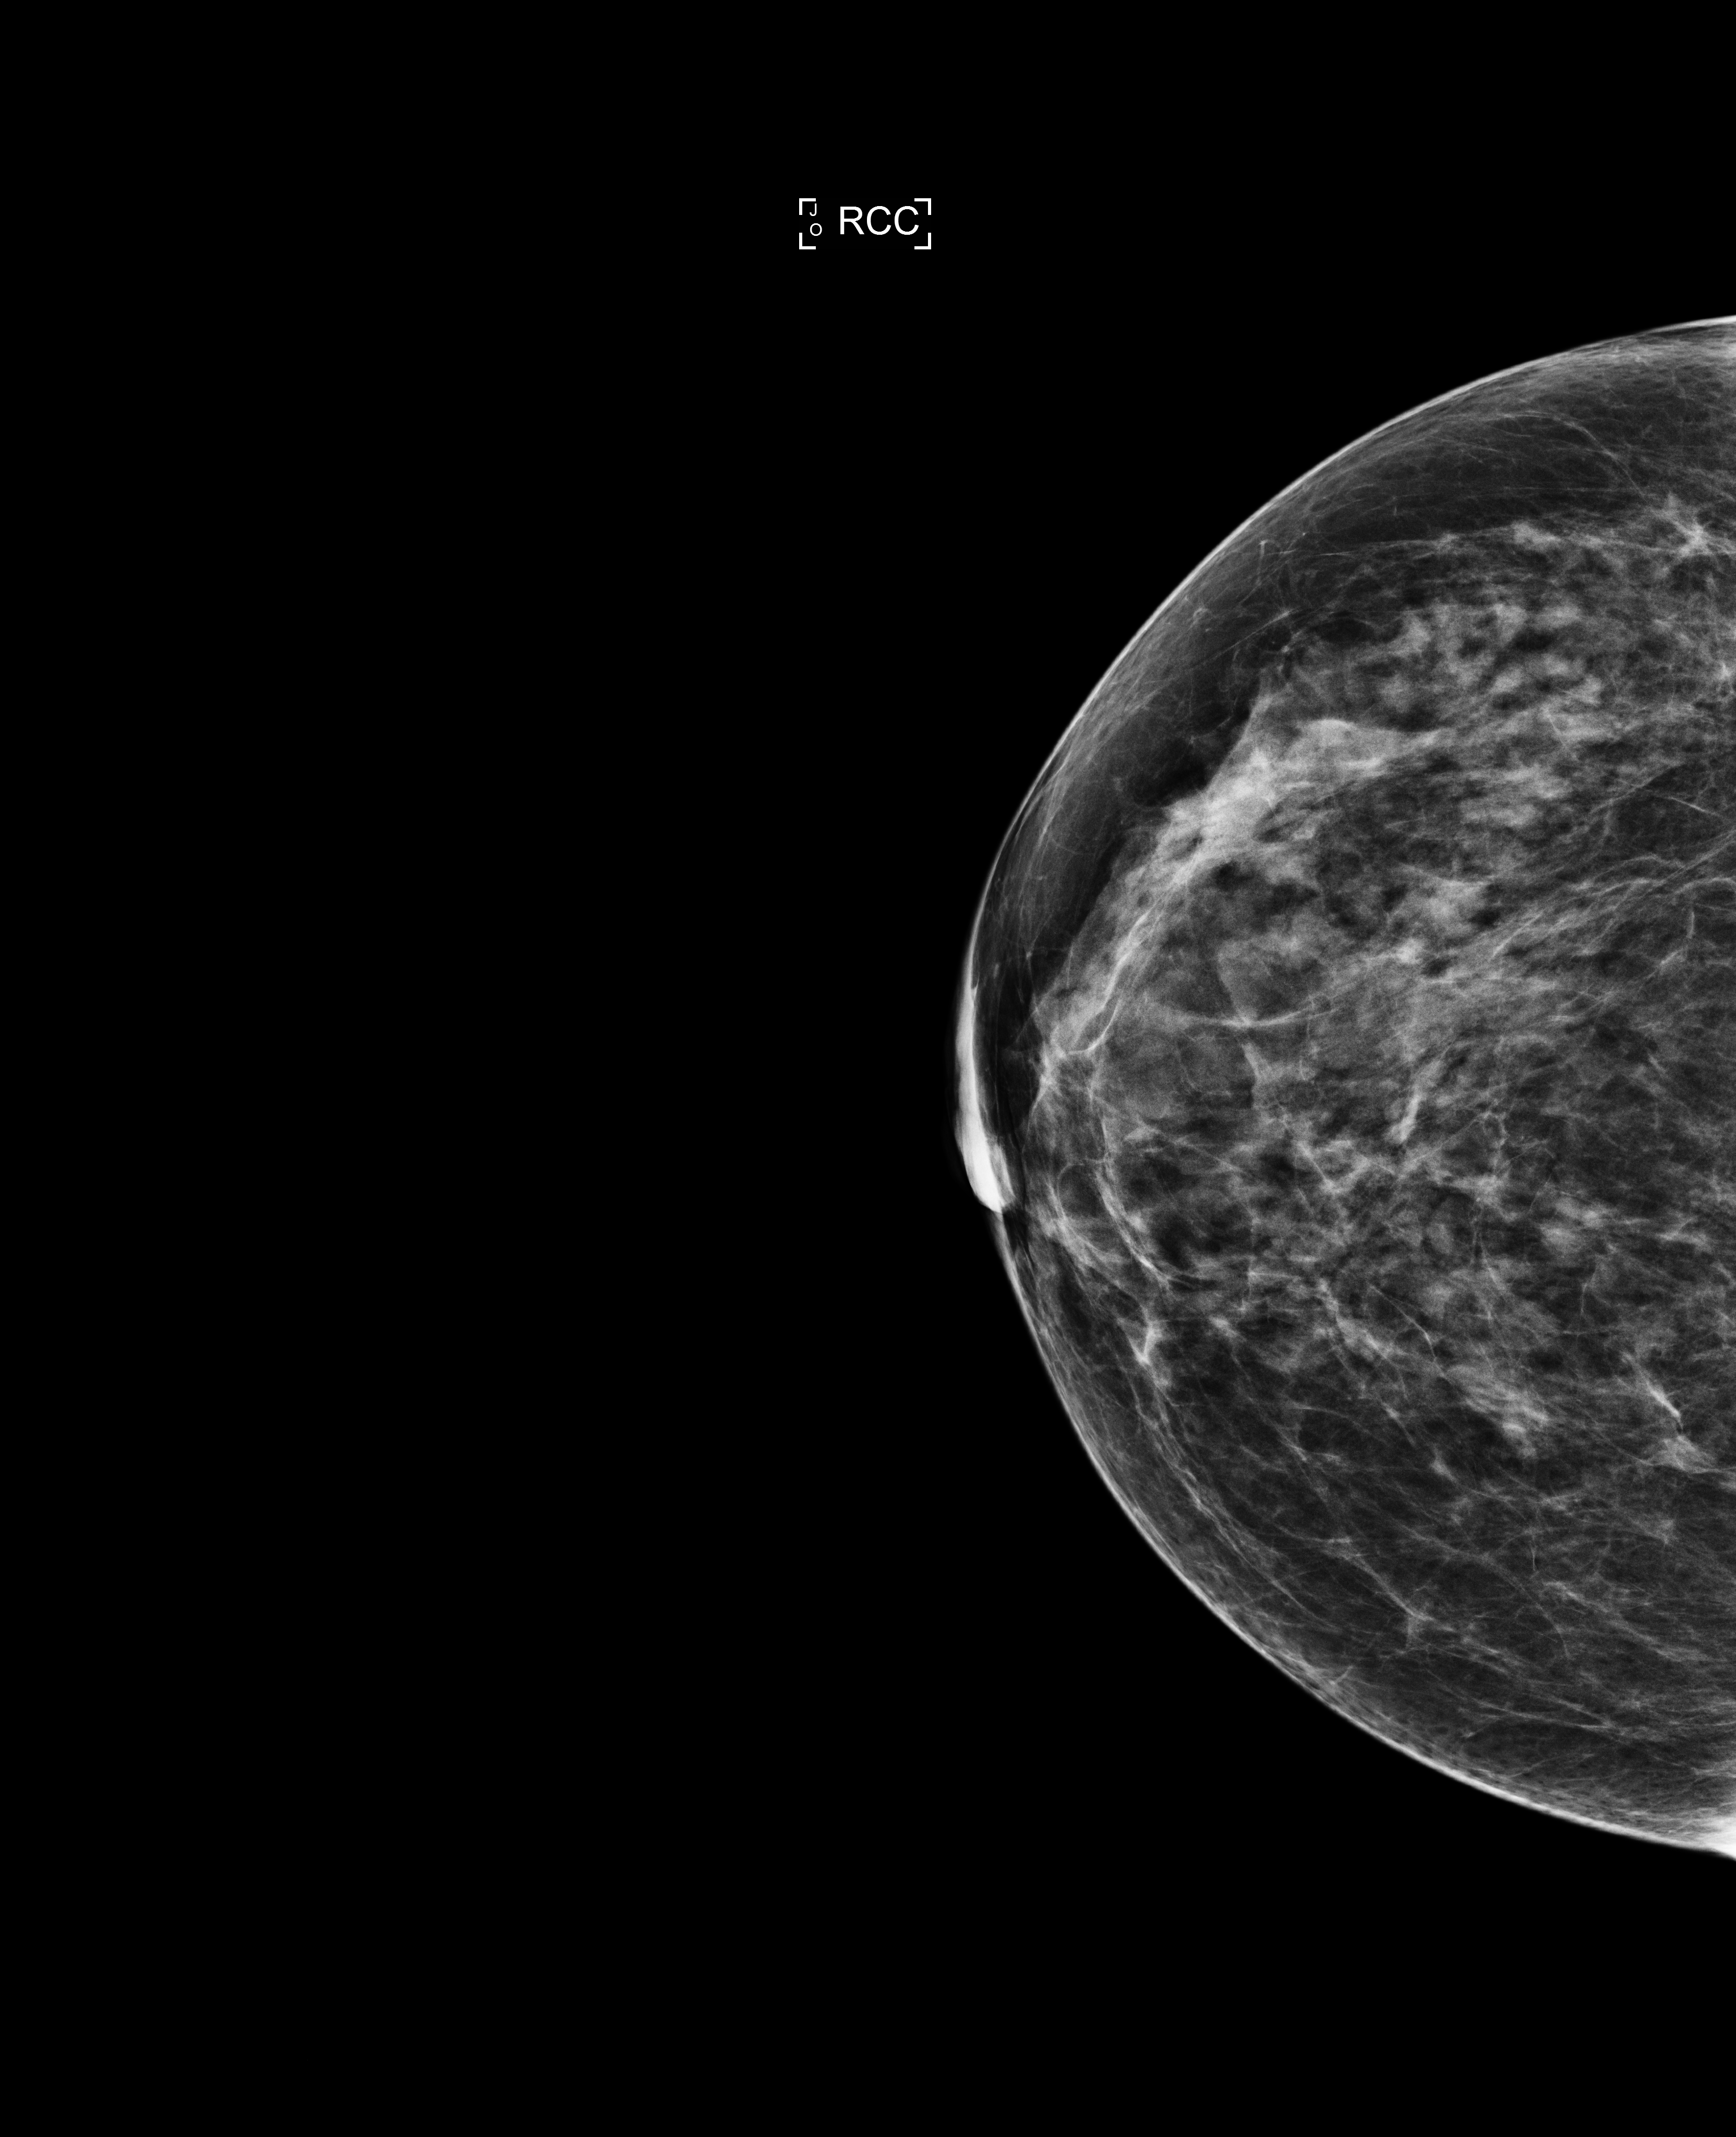
Digital mammogram (FFDM); right breast; craniocaudal (CC) view; annual screening mammography examination. Patient aged 57 years (female).
BI-RADS breast density category at the screening exam (both breasts, scale 1–4): 3. Final BI-RADS category for the screening round (tomosynthesis exam, both breasts): category 1. Recall: no recall after this screen.